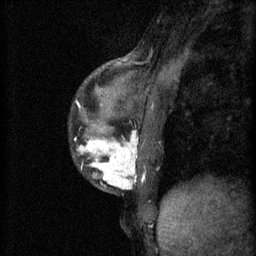
Breast MRI (dynamic contrast-enhanced), one sagittal slice. Slice 23 of 60 in the series (ordered by position). 3 images stored at this slice position (order not interpretable as contrast timing). 1.5 T. TE 4.2 ms, TR 11 ms. 2 mm slice thickness. 256 × 256 image matrix, field of view 180 × 180 mm. Patient: female, 37 years.
Outlined on this slice (semi-automatic segmentation, software-assisted and operator-edited):
- analysis volume of interest (the breast-tissue region the enhancement analysis was run in; not a lesion): bounding box (x1, y1, x2, y2) in pixels: (73, 118, 154, 193)
- tumour enhancement mask (voxels above the 70 % enhancement threshold inside the analysis volume of interest): (78, 132, 138, 189)